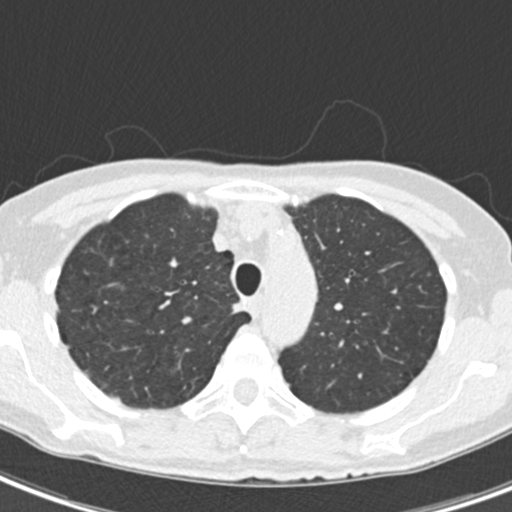
Low-dose screening chest CT, axial slice. Second screening round (one year after baseline). Lung window (W 1500 / L -600 HU). 2 mm slice thickness. 120 kVp. 512 × 512 image matrix. Female participant, aged 68 years at enrolment. Current smoker at enrolment.
Expert-annotated lung lesion, bounding box <225,300,253,325> (left, top, right, bottom; pixels). No non-calcified nodule or mass ≥4 mm was recorded by the screening reader at this exam. Later outcome: lung cancer diagnosed 436 days after this screen — squamous cell carcinoma, NOS, right upper lobe, mediastinum, poorly differentiated (G3), stage IIIB (AJCC 6th edition), 43 mm at pathology.